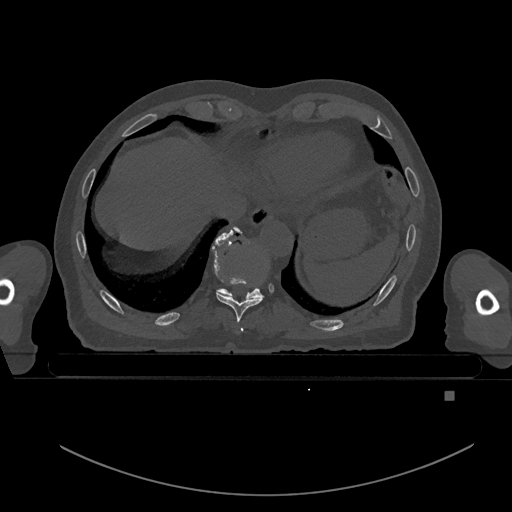
CT including the spine, one axial slice; position 127 of 969 along the scan axis; bone window (W 1800 / L 400 HU); 0.5 mm slice thickness; 512 × 512 image matrix, field of view 456 × 456 mm. Patient: male, 82 years. From the clinical record (not read from this slice): primary cancer: prostate.
Structures marked on this image (semi-automatic segmentation, software-assisted and operator-edited):
- T10 vertebra: bounding box [x1, y1, x2, y2] px = [218, 226, 261, 298]
- T9 vertebra: [212, 230, 264, 331]